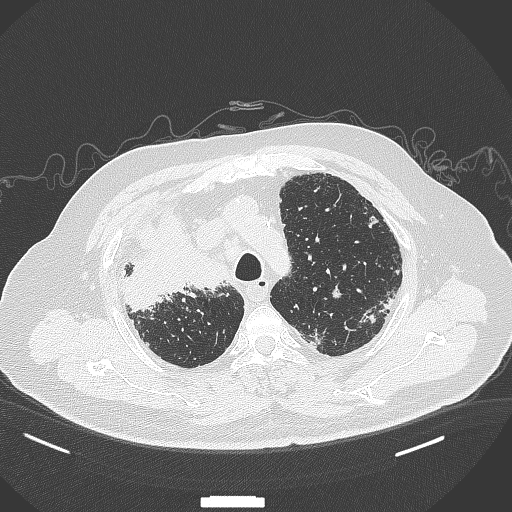
Chest CT, one axial slice. Slice 283 of 384 in the series (ordered by position). 120 kVp. Lung window (W 1500 / L -600 HU). 1 mm slice thickness. 512 × 512 image matrix, field of view 400 × 400 mm. Male patient, age 69 years. From the clinical record (not read from this slice): clinical TNM (as recorded): T4 N3 M1.
Annotated regions visible in this slice (bounding box drawn by a radiologist):
- lung tumour (recorded histology: adenocarcinoma): bounding box [x1, y1, x2, y2] px = [115, 210, 230, 313]